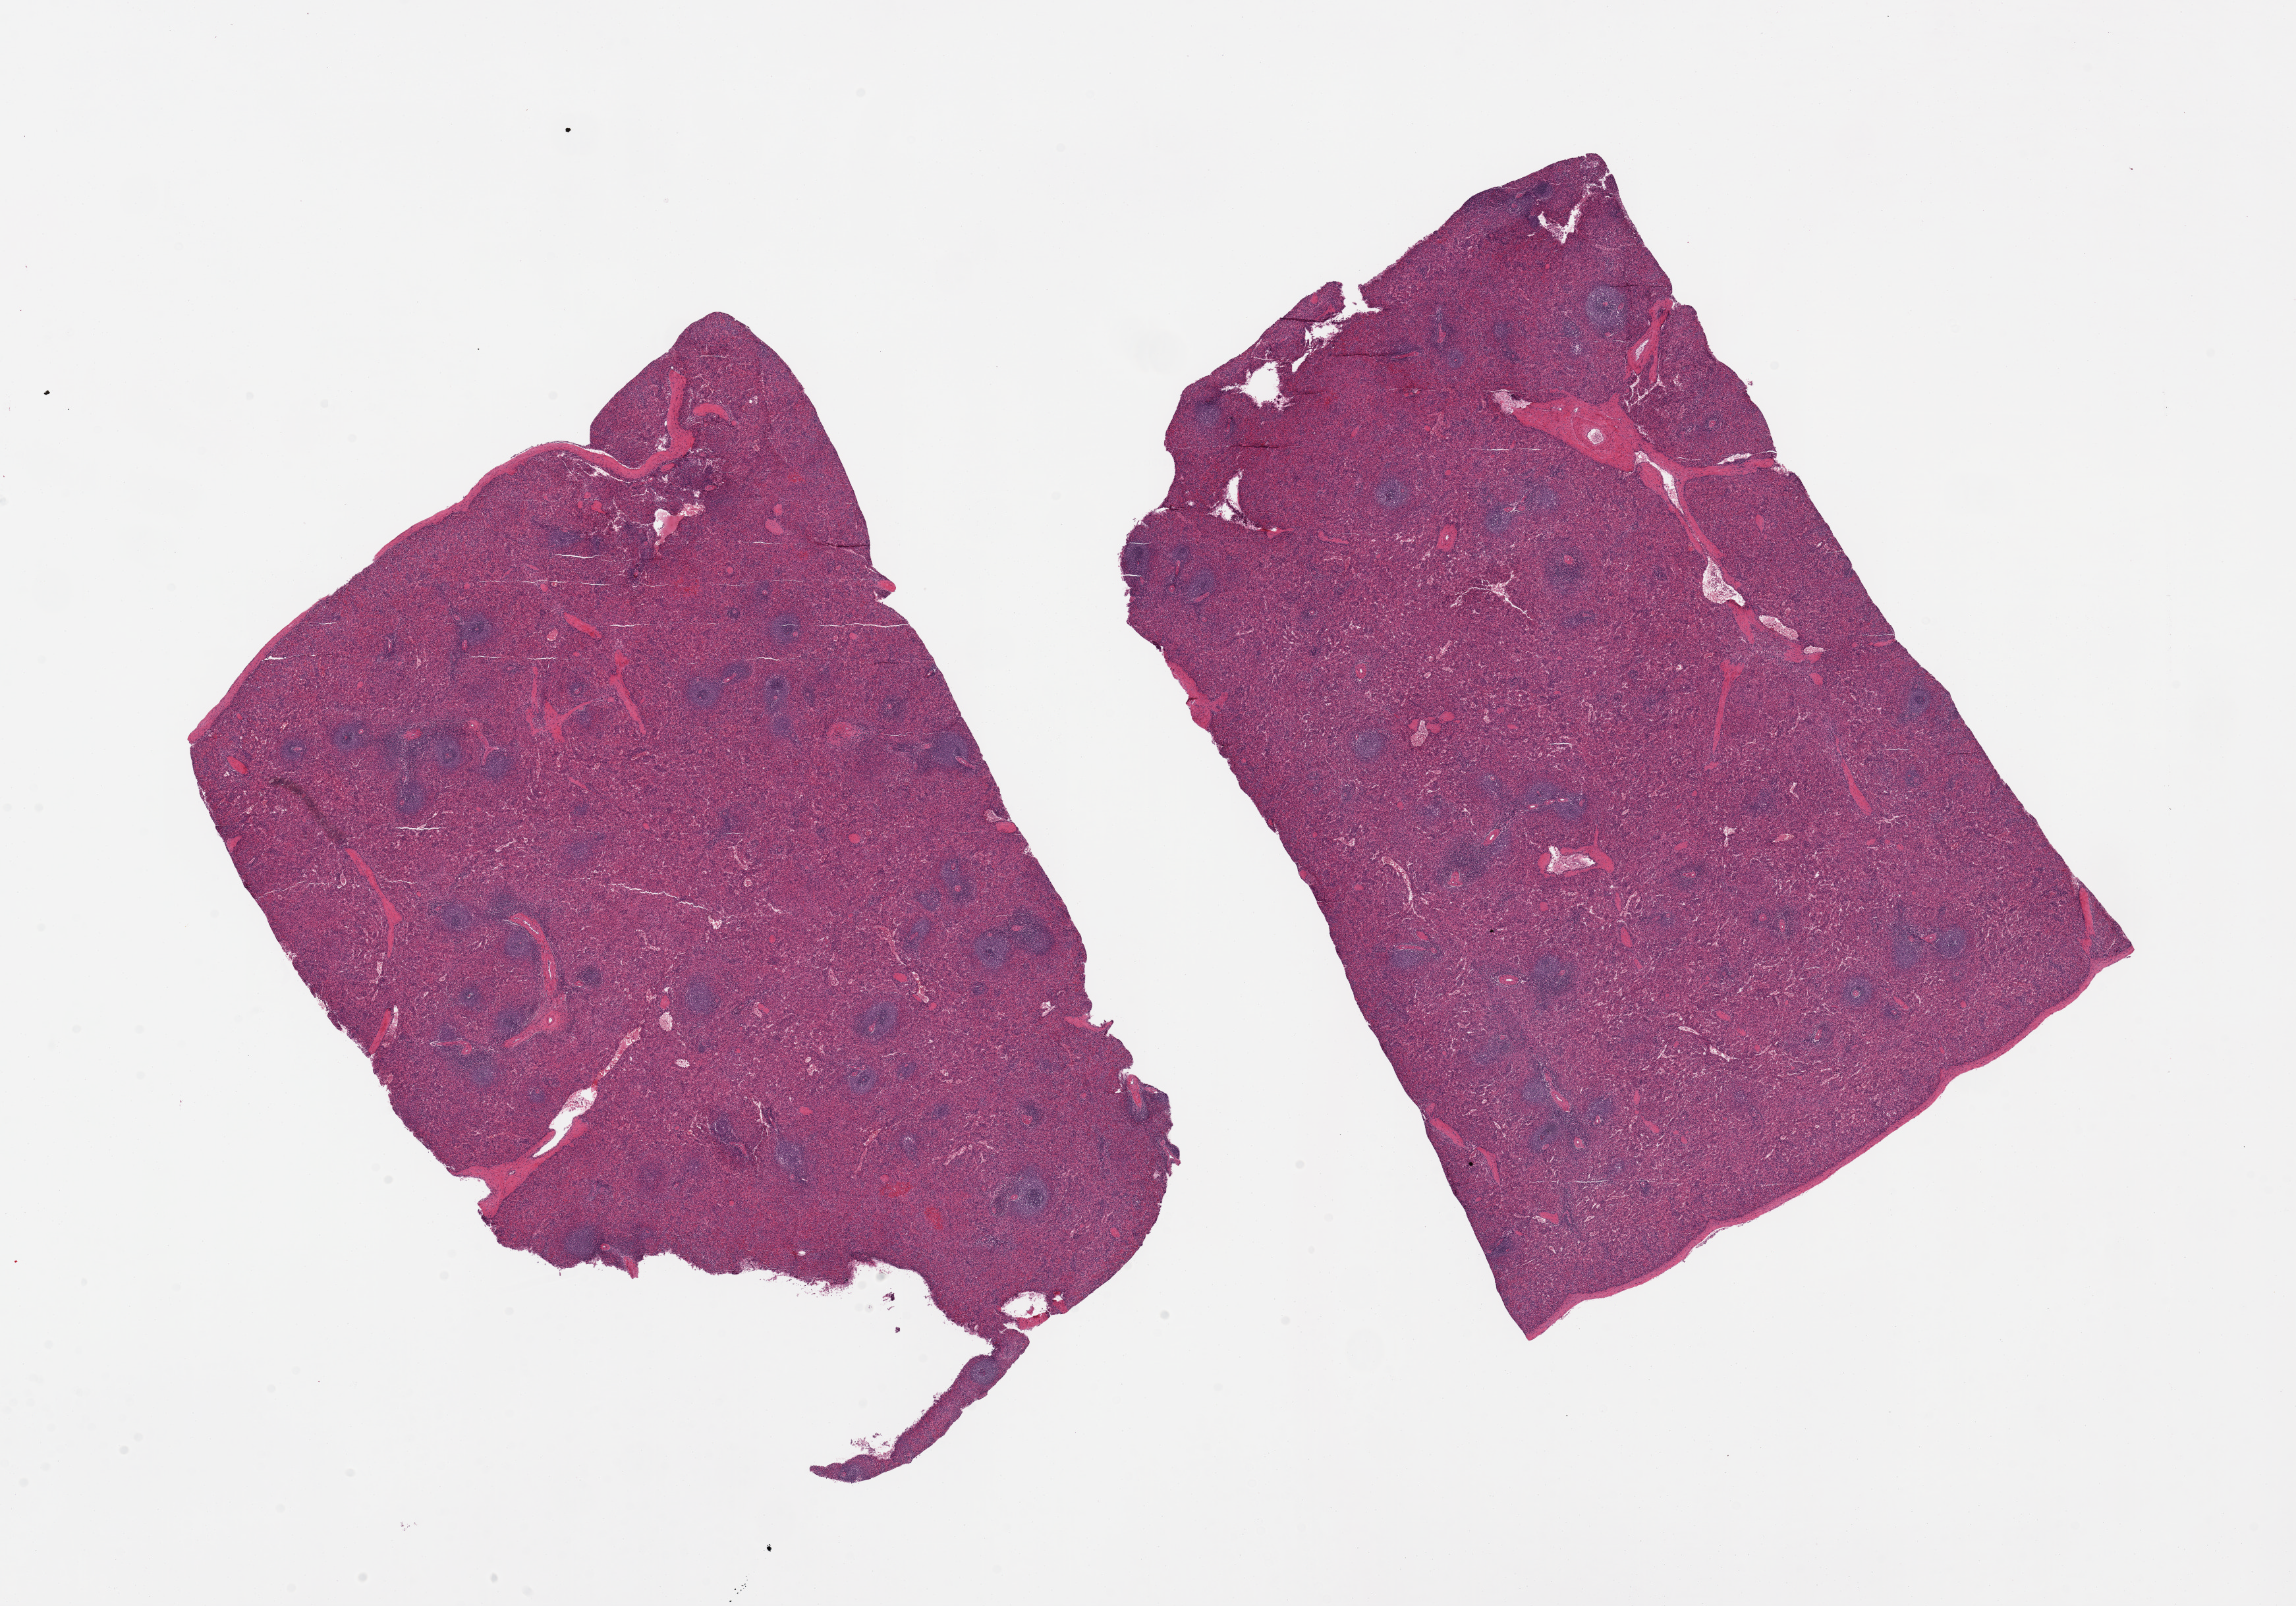
Digitized hematoxylin and eosin (H&E)-stained section, brightfield, low-resolution overview of the scanned area, about 27.6 x 19.3 mm. PAXgene-fixed, paraffin-embedded tissue. Sampled site (target tissue): spleen. Donor tissue sample. Donor: male.
Pathologist's review note for this sample: 2 pieces. 12.5x9 & 12x9mm.